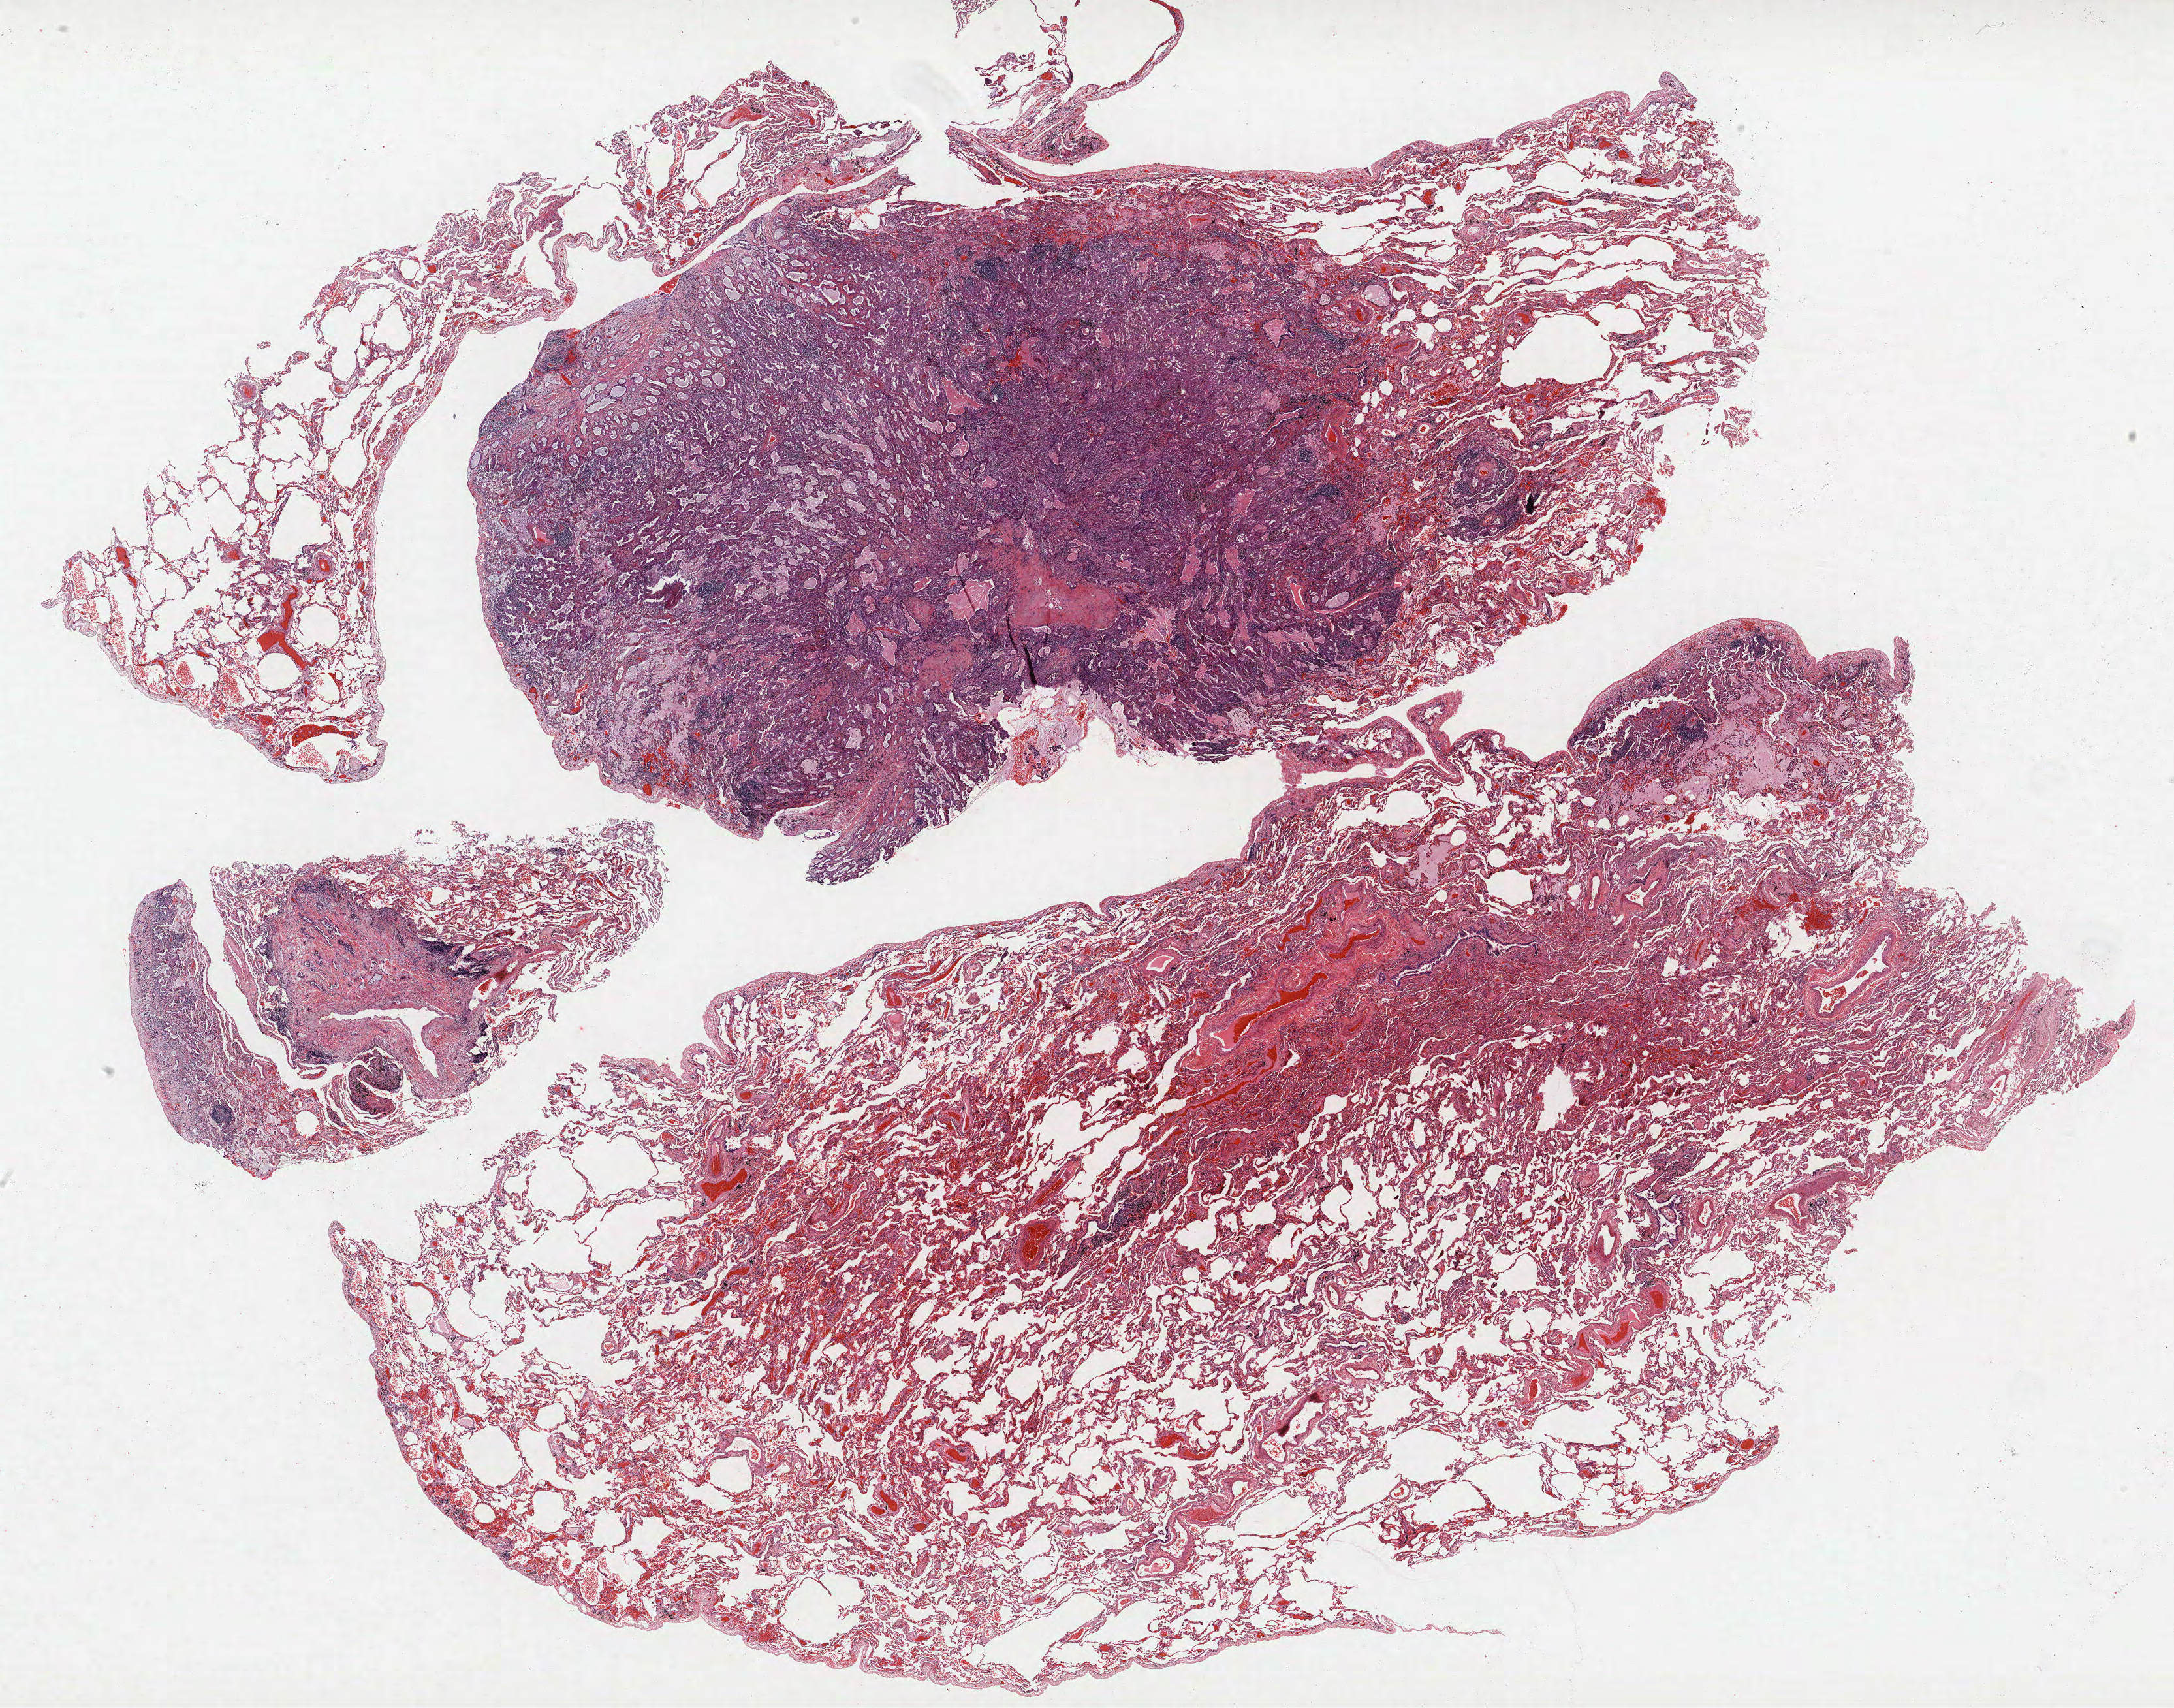
Hematoxylin and eosin (H&E) stained whole-slide image, shown as a low-resolution overview of the whole scanned area (about 26.6 x 20.9 mm, slide scanned at 40x), formalin-fixed paraffin-embedded (FFPE) section, lung tissue. Female patient, aged 68 at enrolment. Former smoker at enrolment. Grade: well differentiated (G1).
Stage (AJCC 6th edition): IV. Participant's lung-cancer diagnosis: Bronchiolo-alveolar adenocarcinoma, NOS. Primary tumour location (clinical record): right upper lobe, right middle lobe, right lower lobe.